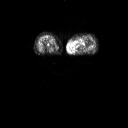
FDG PET of an extremity soft-tissue mass (from a PET/CT study), one axial slice; position 8 of 91 along the scan axis; 3.27 mm slice thickness; 128 × 128 image matrix, field of view 700 × 700 mm. Patient: female, 74 years. Case-level facts recorded for this patient, not image findings: histological type: pleomorphic leiomyosarcoma; grade: high; site of the primary tumour: left thigh.
Structures marked on this image (expert contour drawn on MRI and transferred to this co-registered scan by the dataset authors):
- gross tumour volume including surrounding oedema: bounding box <72,38,87,50> (left, top, right, bottom; pixels)